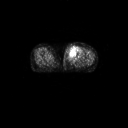
FDG PET of an extremity soft-tissue mass (from a PET/CT study), one axial slice. Position 43 of 91 along the scan axis. 3.27 mm slice thickness. 128 × 128 image matrix, field of view 700 × 700 mm. Patient: female, 74 years. From the clinical record (not read from this slice): histological type: pleomorphic leiomyosarcoma; grade: high; site of the primary tumour: left thigh.
Structures marked on this image (expert contour drawn on MRI and transferred to this co-registered scan by the dataset authors):
- gross tumour volume including surrounding oedema: bounding box [x1, y1, x2, y2] px = [65, 46, 80, 61]
- gross tumour volume (mass): [68, 46, 78, 58]